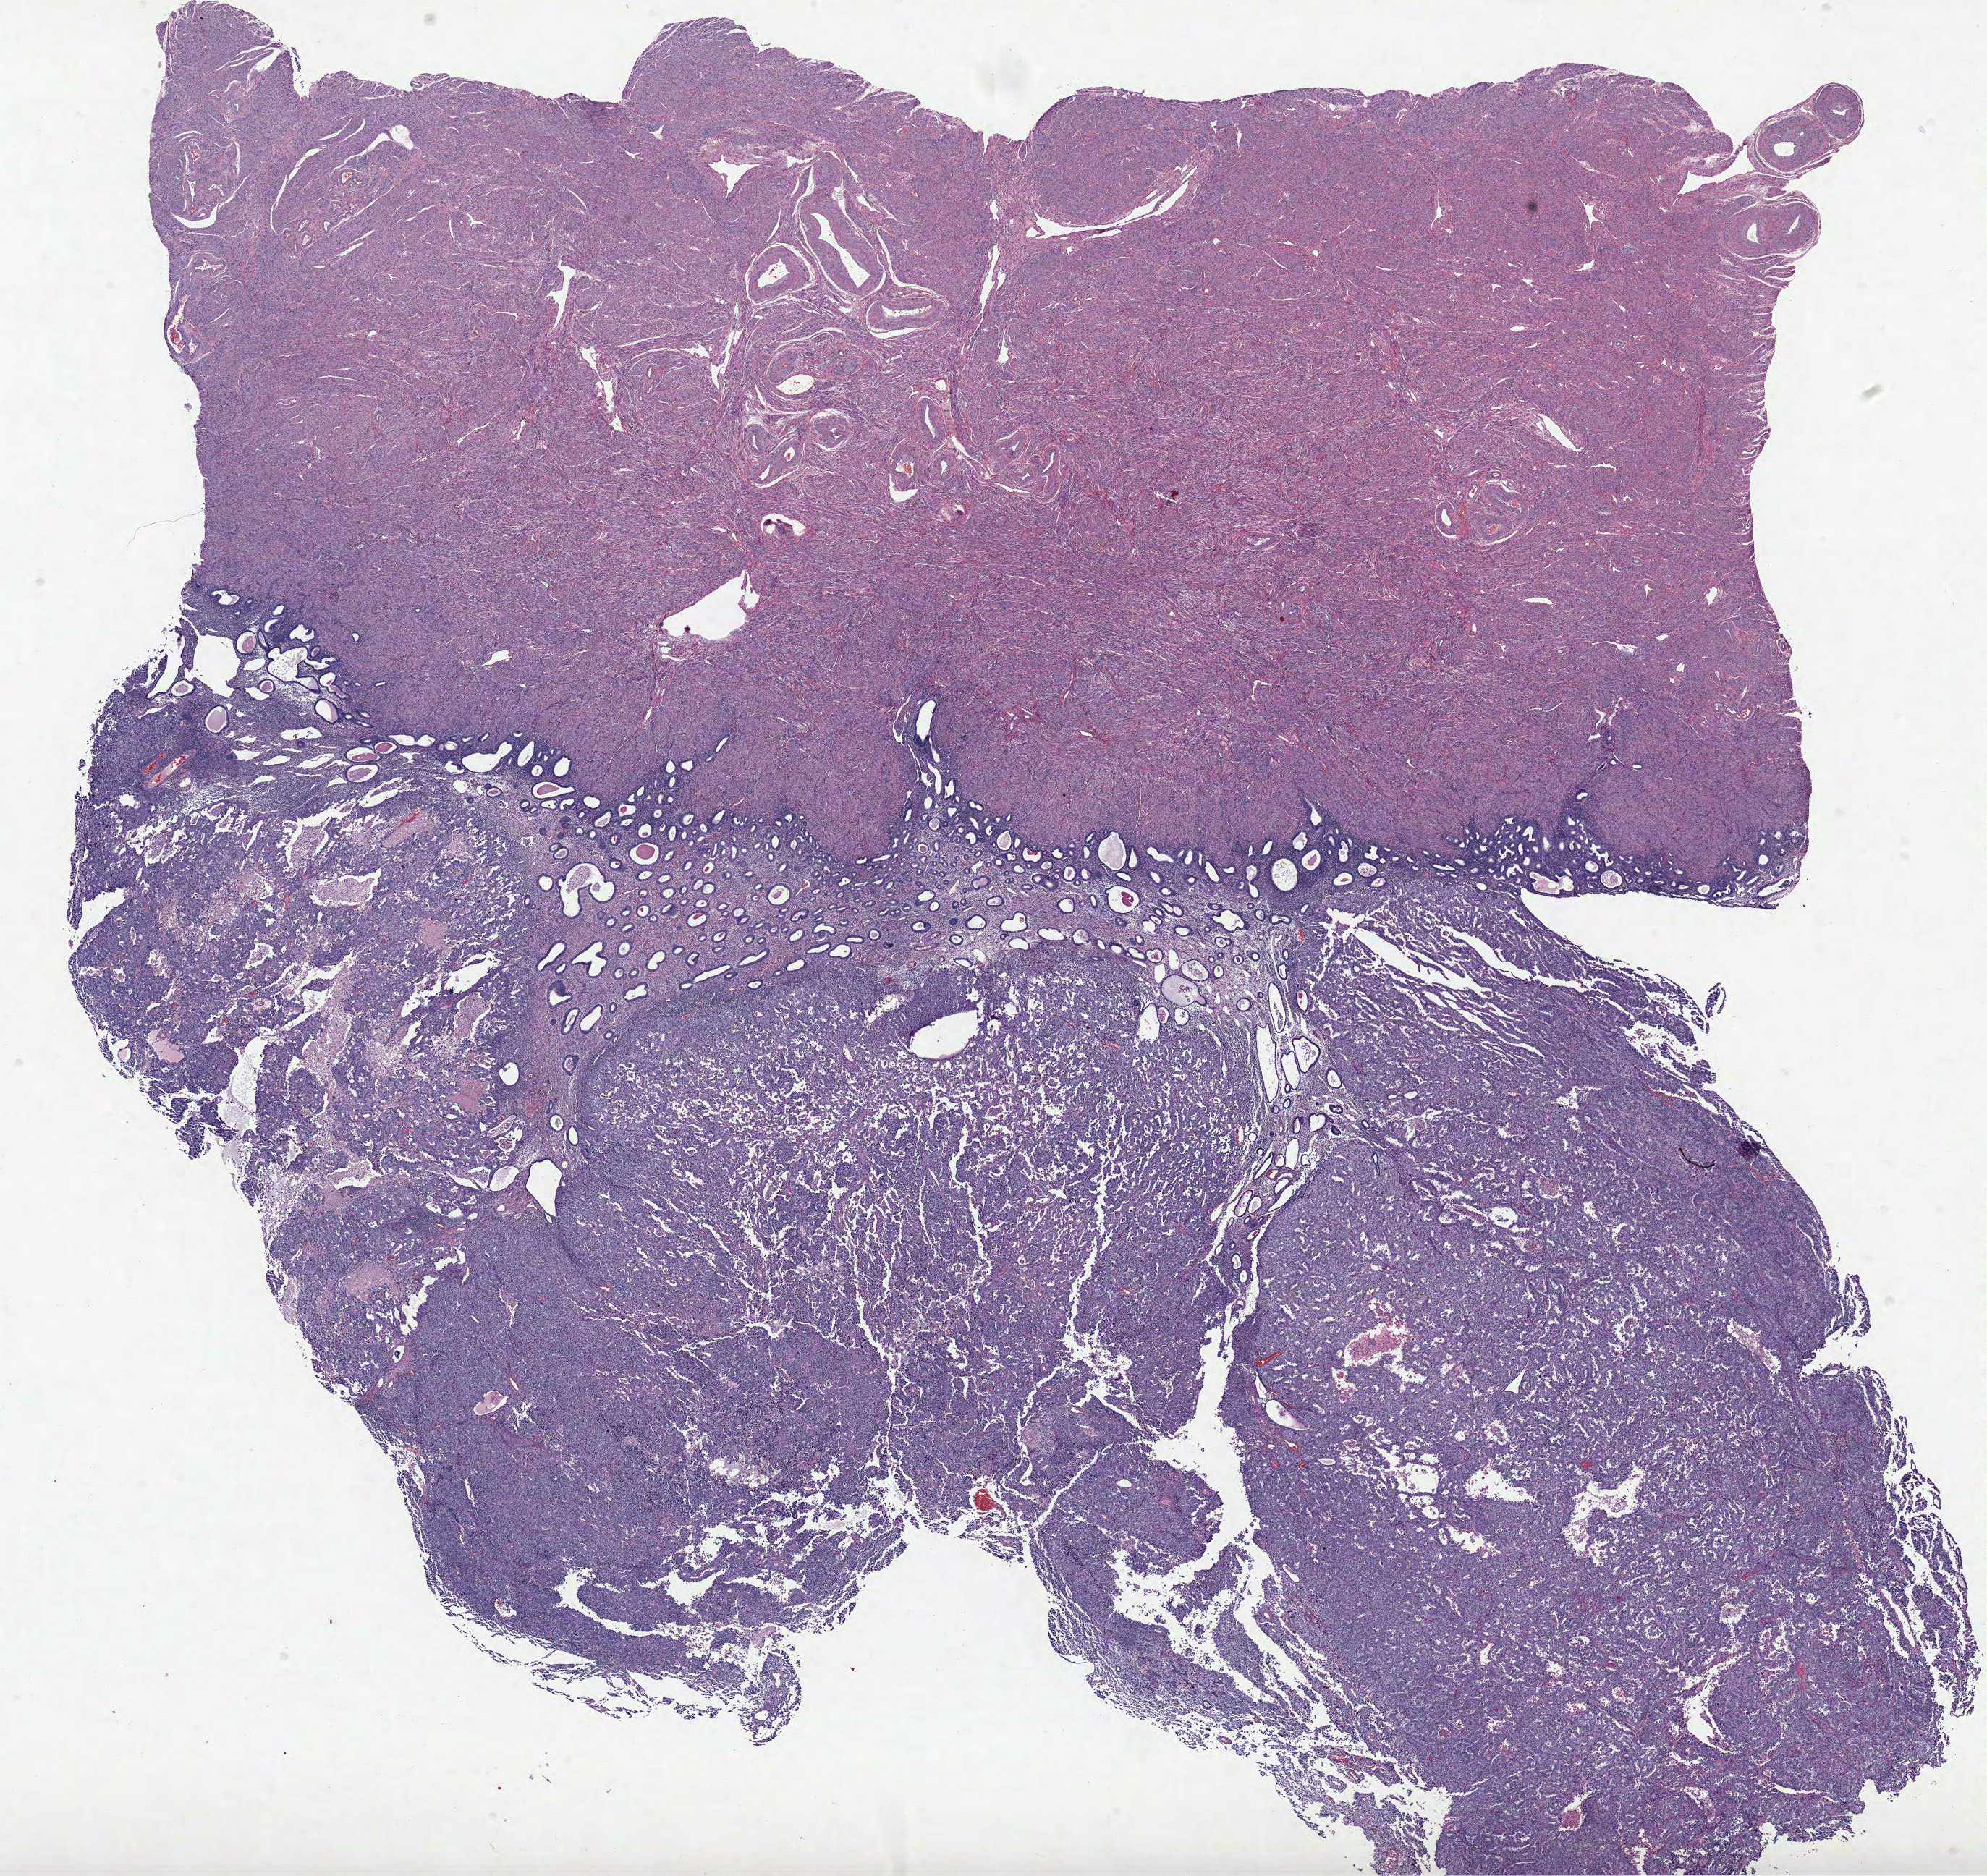
Whole-slide histology image, H&E-stained, low-resolution overview of the scanned area, about 21.9 x 20.7 mm. FFPE section. Sample: primary tumour, uterus. Patient: female, age at initial diagnosis 71 years. Histologic grade: G3 (poorly differentiated).
Diagnosis: Serous cystadenocarcinoma, NOS. FIGO stage: IA.